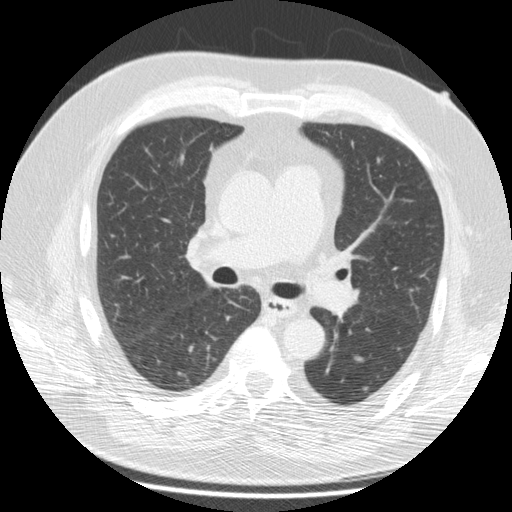
Low-dose screening chest CT, one axial slice. Slice 104 of 172 in the series (ordered by position). Reconstruction kernel STANDARD. 120 kVp. Lung window (W 1500 / L -600 HU). 2.5 mm slice thickness. 512 × 512 image matrix, field of view 364 × 364 mm.
Outlined on this slice (outlined manually by an expert reader):
- lesion 1 (tumor, lower lobe of left lung): bounding box (x1, y1, x2, y2) in pixels: (362, 385, 370, 394)